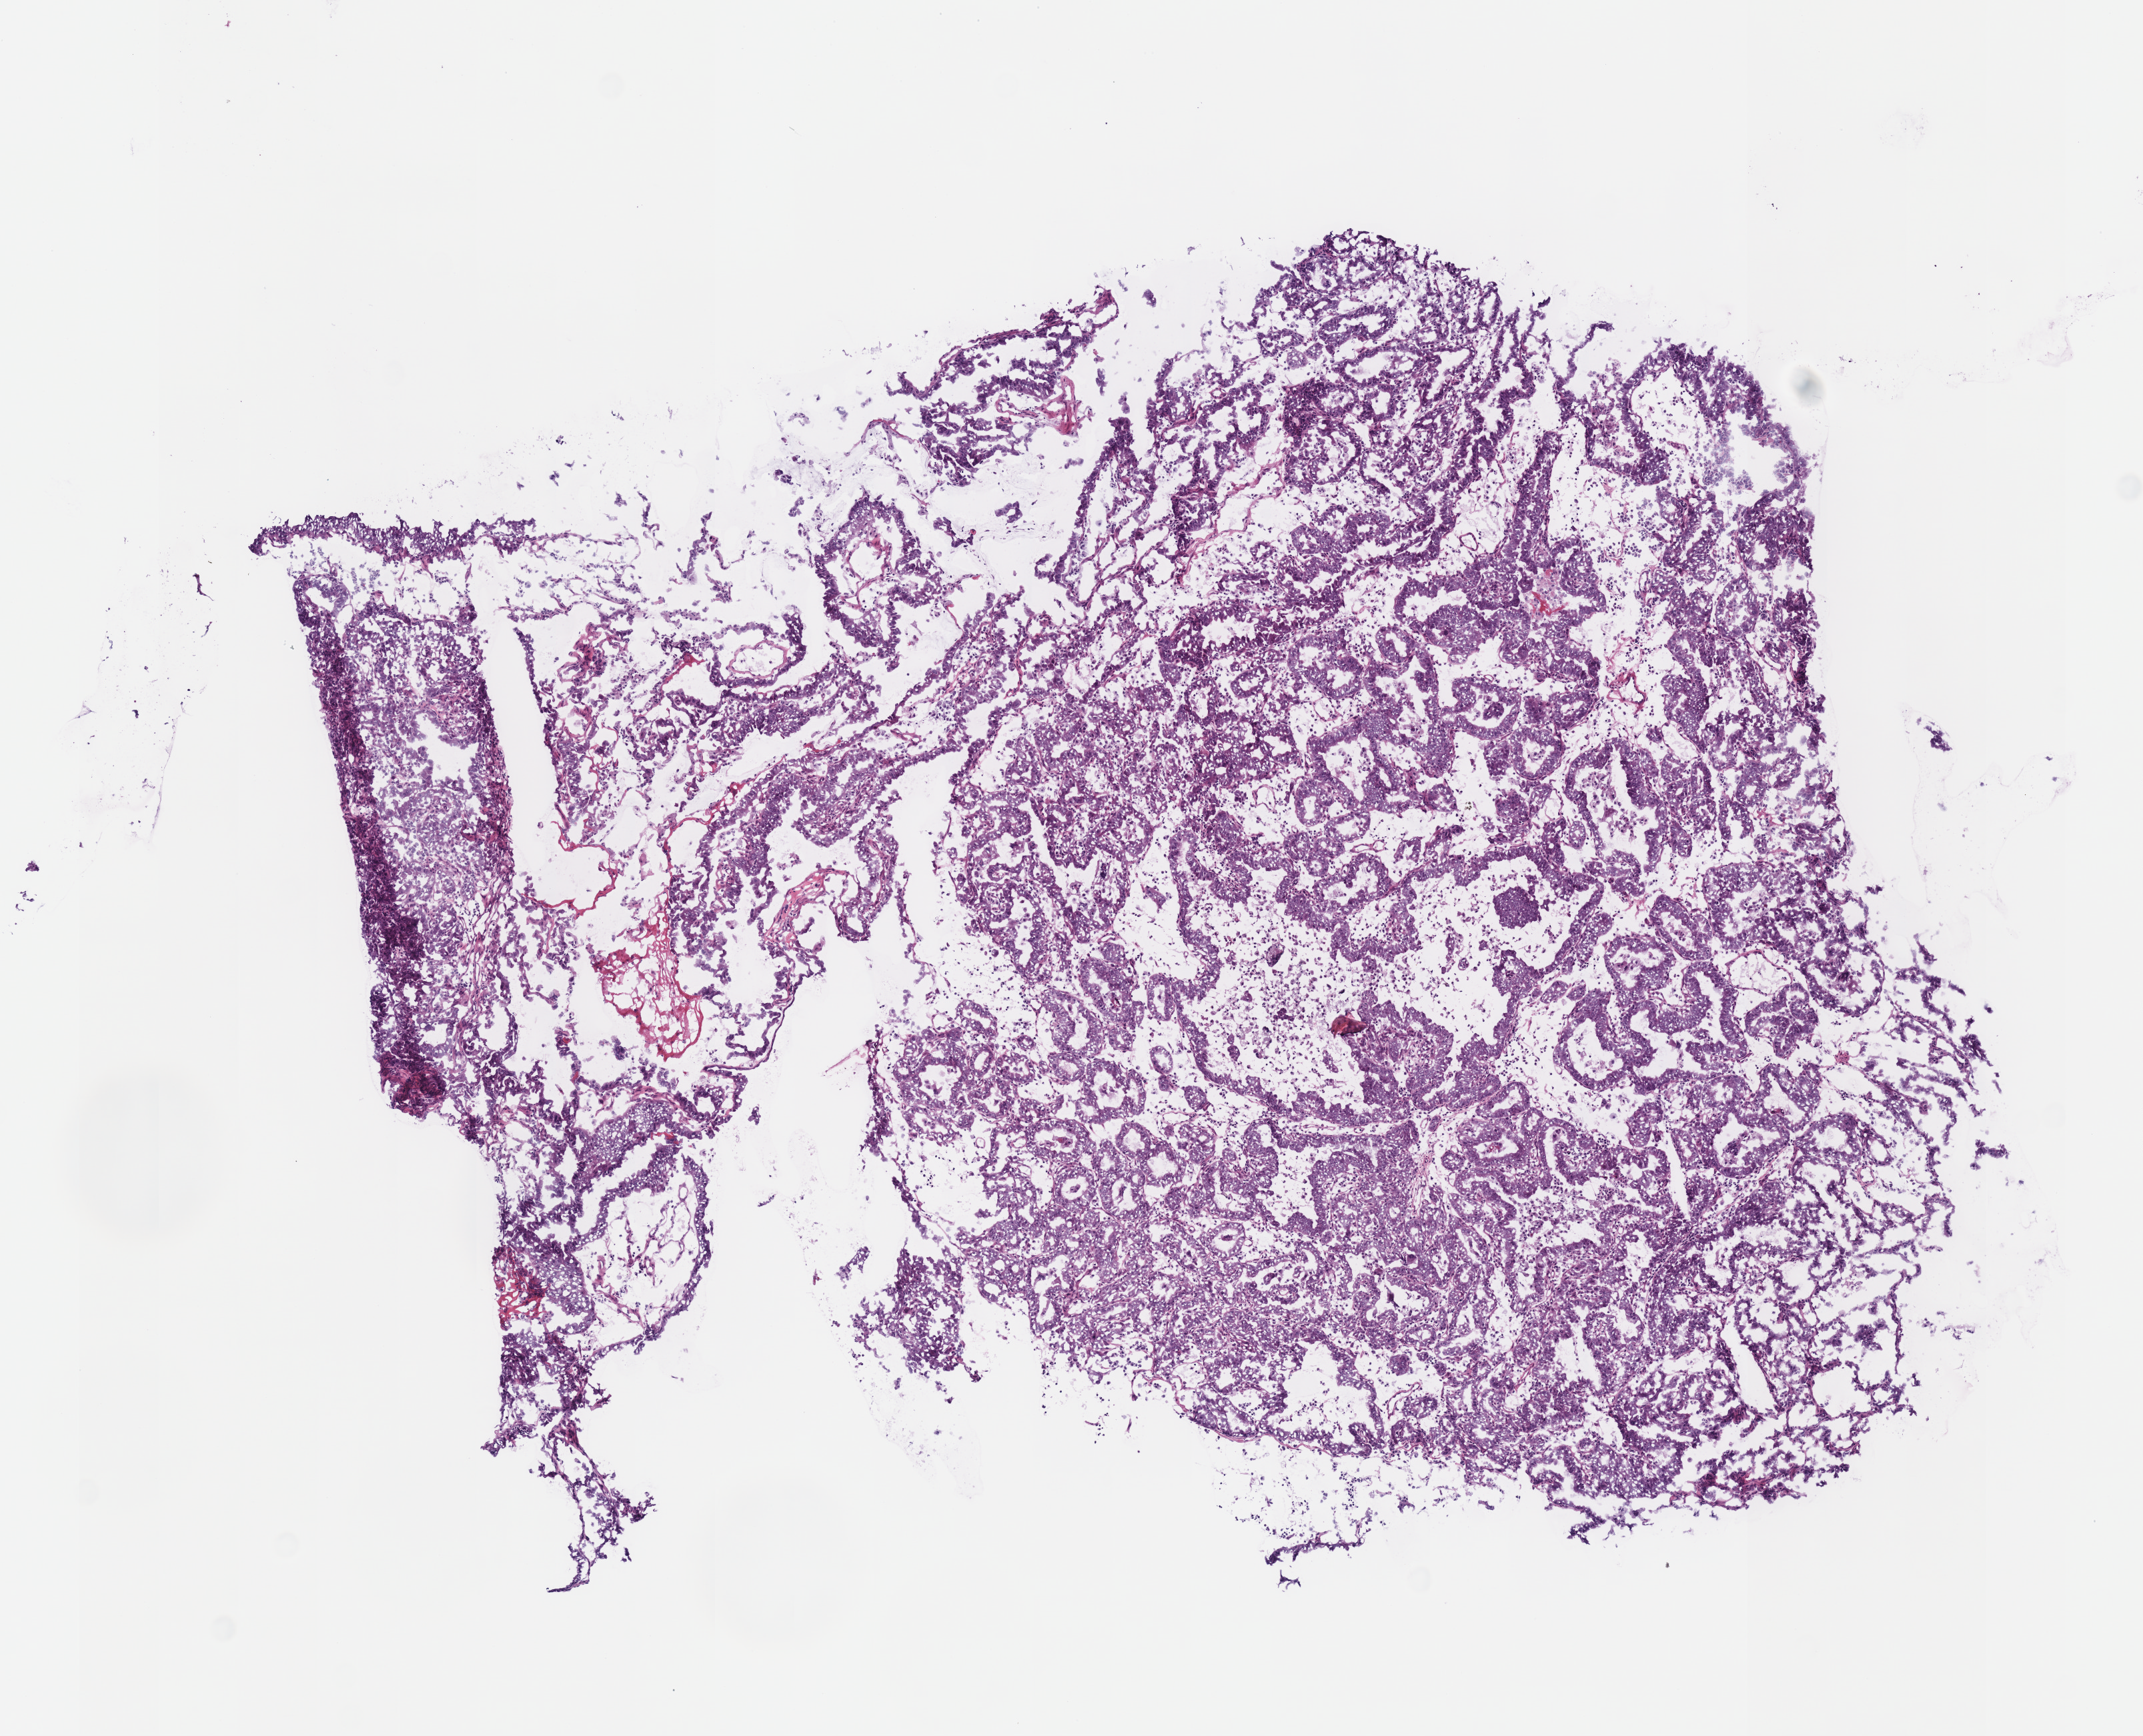
H&E whole-slide image — shown as a low-resolution overview of the whole scanned area (about 6.3 x 5.1 mm, acquisition: 40x scan); frozen section from the top of the tissue portion; stomach, primary tumour sample. Male, age 72 years at initial diagnosis. Slide review estimates, as recorded: tumour cells 90%, tumour nuclei 85%.
Pathologic diagnosis: Papillary adenocarcinoma, NOS (body of stomach).